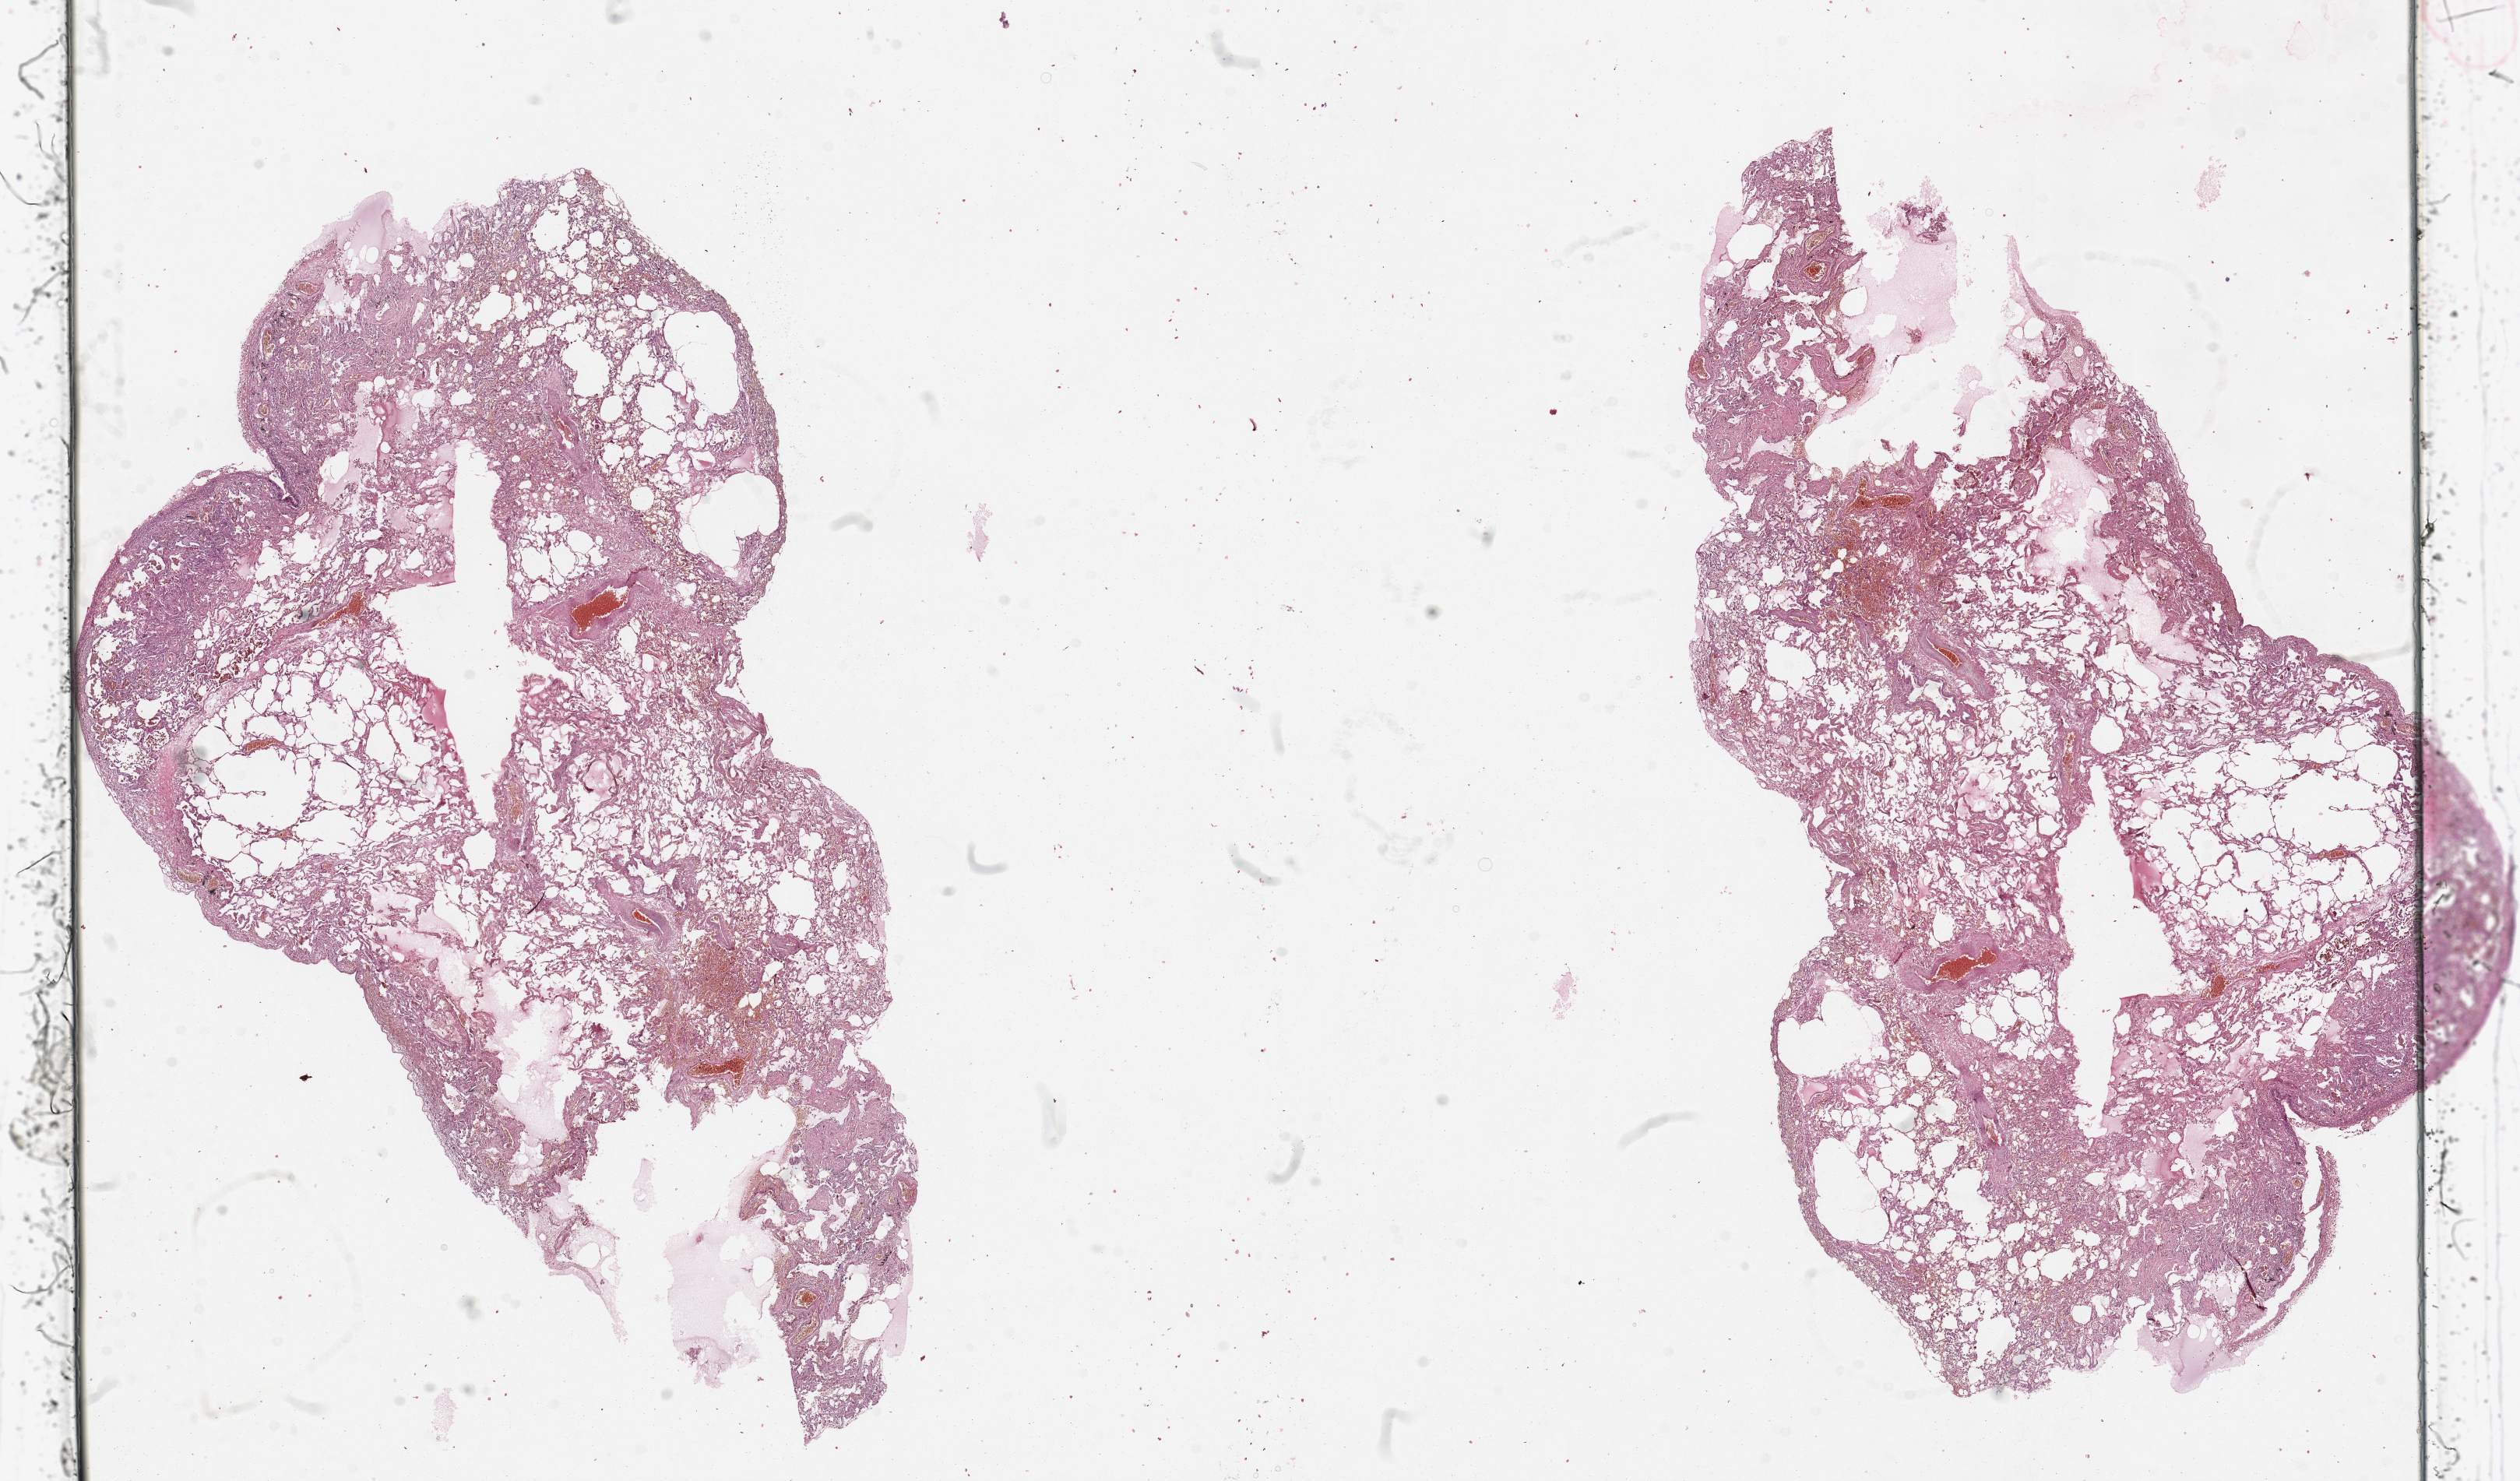
Whole-slide histology image, Hematoxylin and eosin (H&E) stained — whole scanned area (about 25.6 x 15.0 mm, slide scanned at 20x) shown as a low-resolution overview, normal (non-tumour) tissue sample, sampled site: lung. Patient: male, age 47 years.
* this section: normal (non-tumour) tissue from the same patient
* patient diagnosis: Adenocarcinoma, NOS